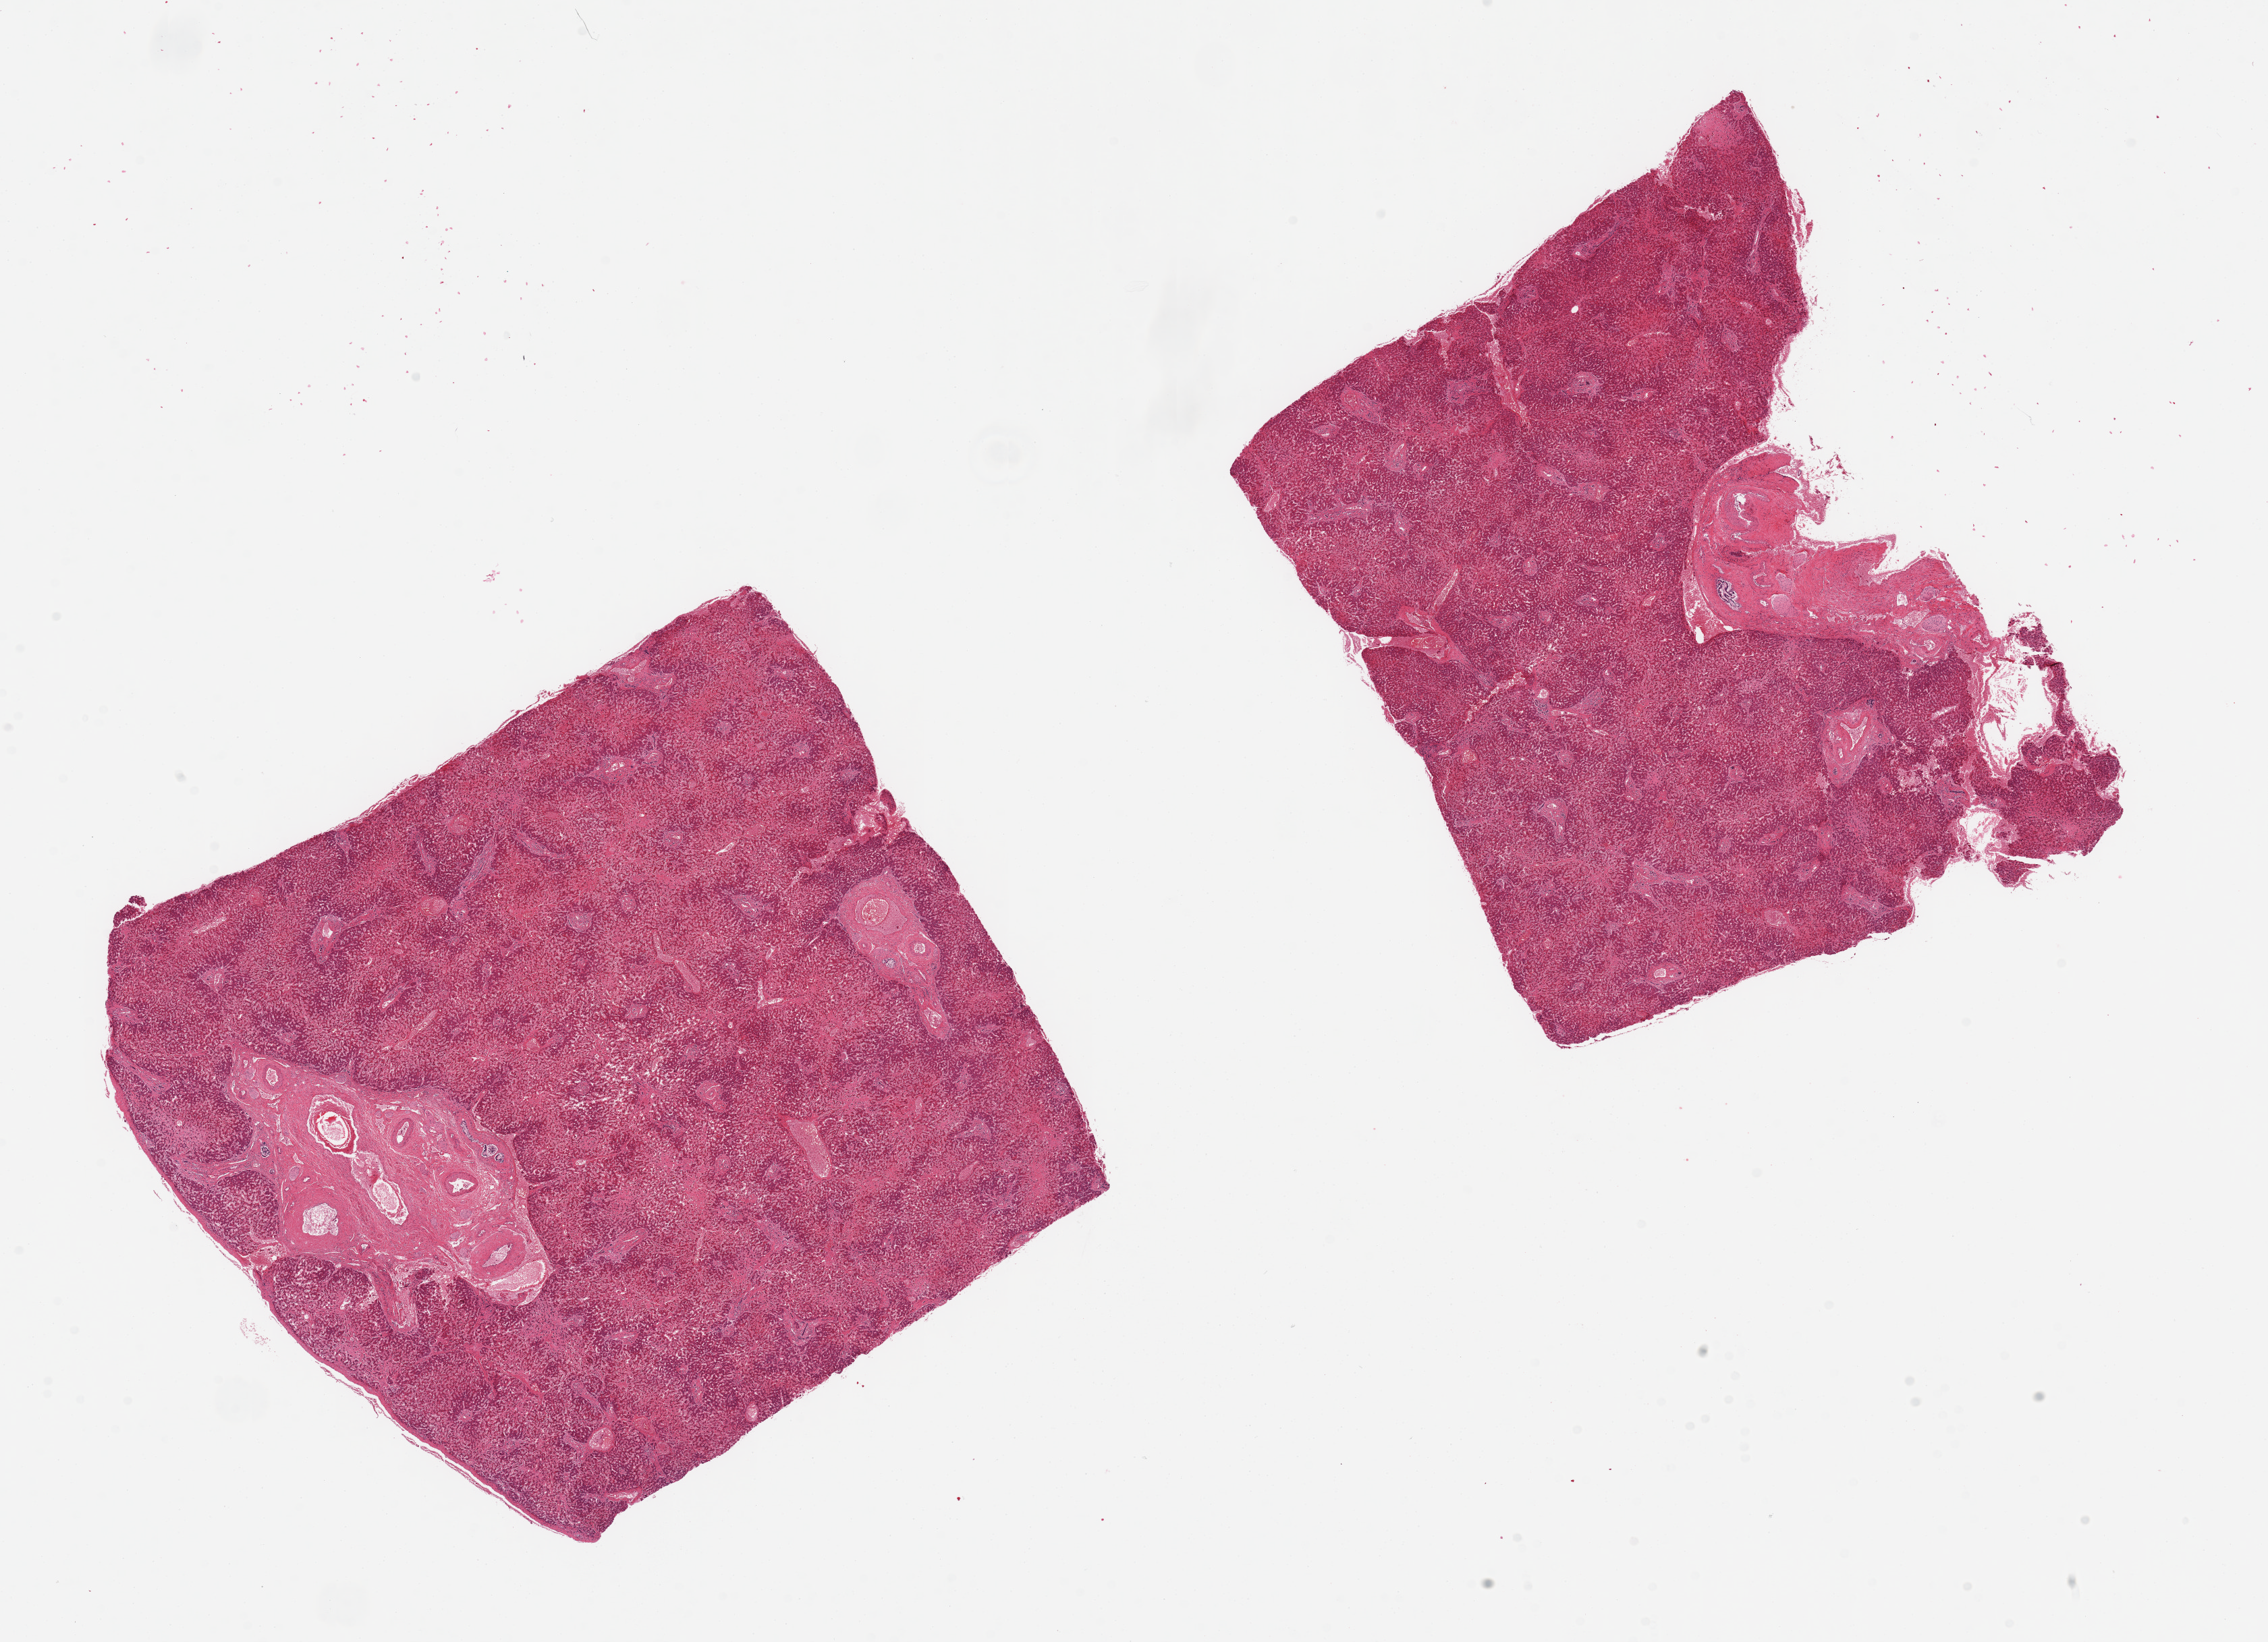
Digitized hematoxylin and eosin (H&E)-stained section — low-resolution overview of the scanned area, about 26.6 x 19.2 mm, PAXgene-fixed, paraffin-embedded tissue, target tissue: liver, tissue donor sample. Donor: male.
• reviewer comment on this tissue sample: 2 pieces; moderate fibrosis, but no nodular cirrhosis; each has focal 5 and 8 sqmm large vessels